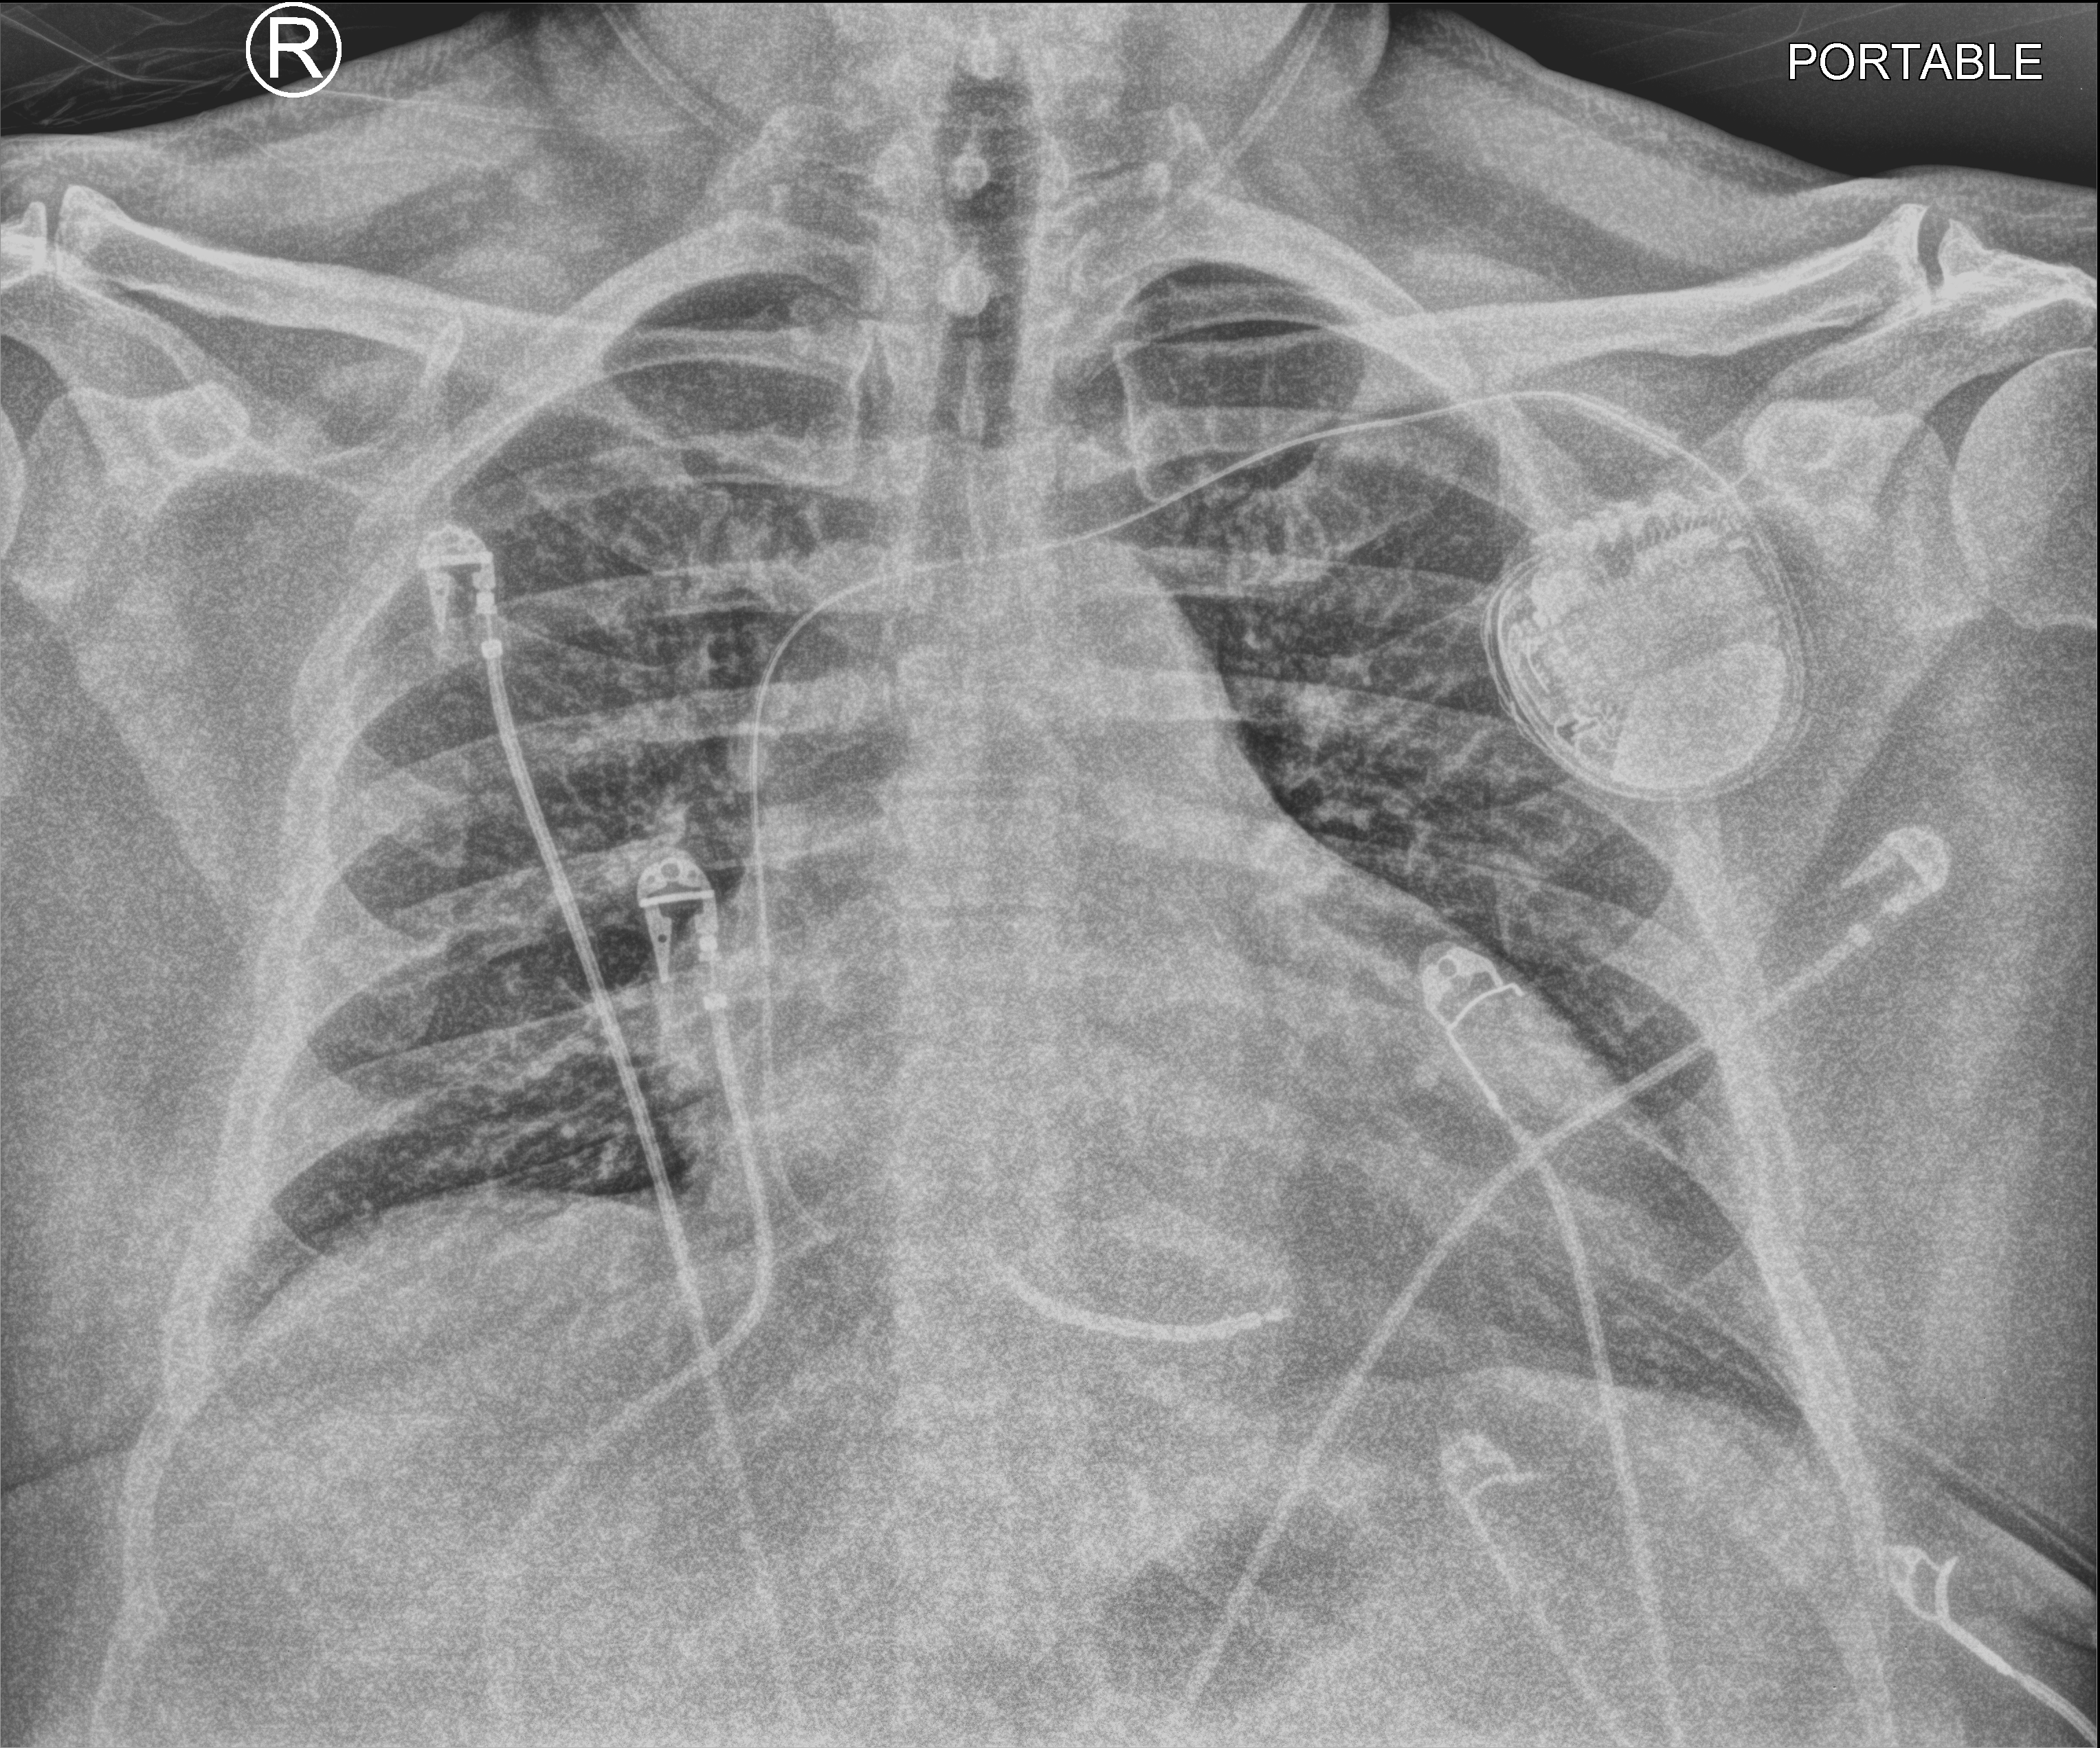
Bedside chest radiograph (computed radiography), anteroposterior (AP) projection. Male patient hospitalised with COVID-19, age 18–59 years.
Hospital-stay facts (about this admission, not read from this image; timing relative to this image not recorded): chronic kidney disease (admission record): no; admitted to intensive care during this hospital stay: yes; length of hospital stay: 4 days.